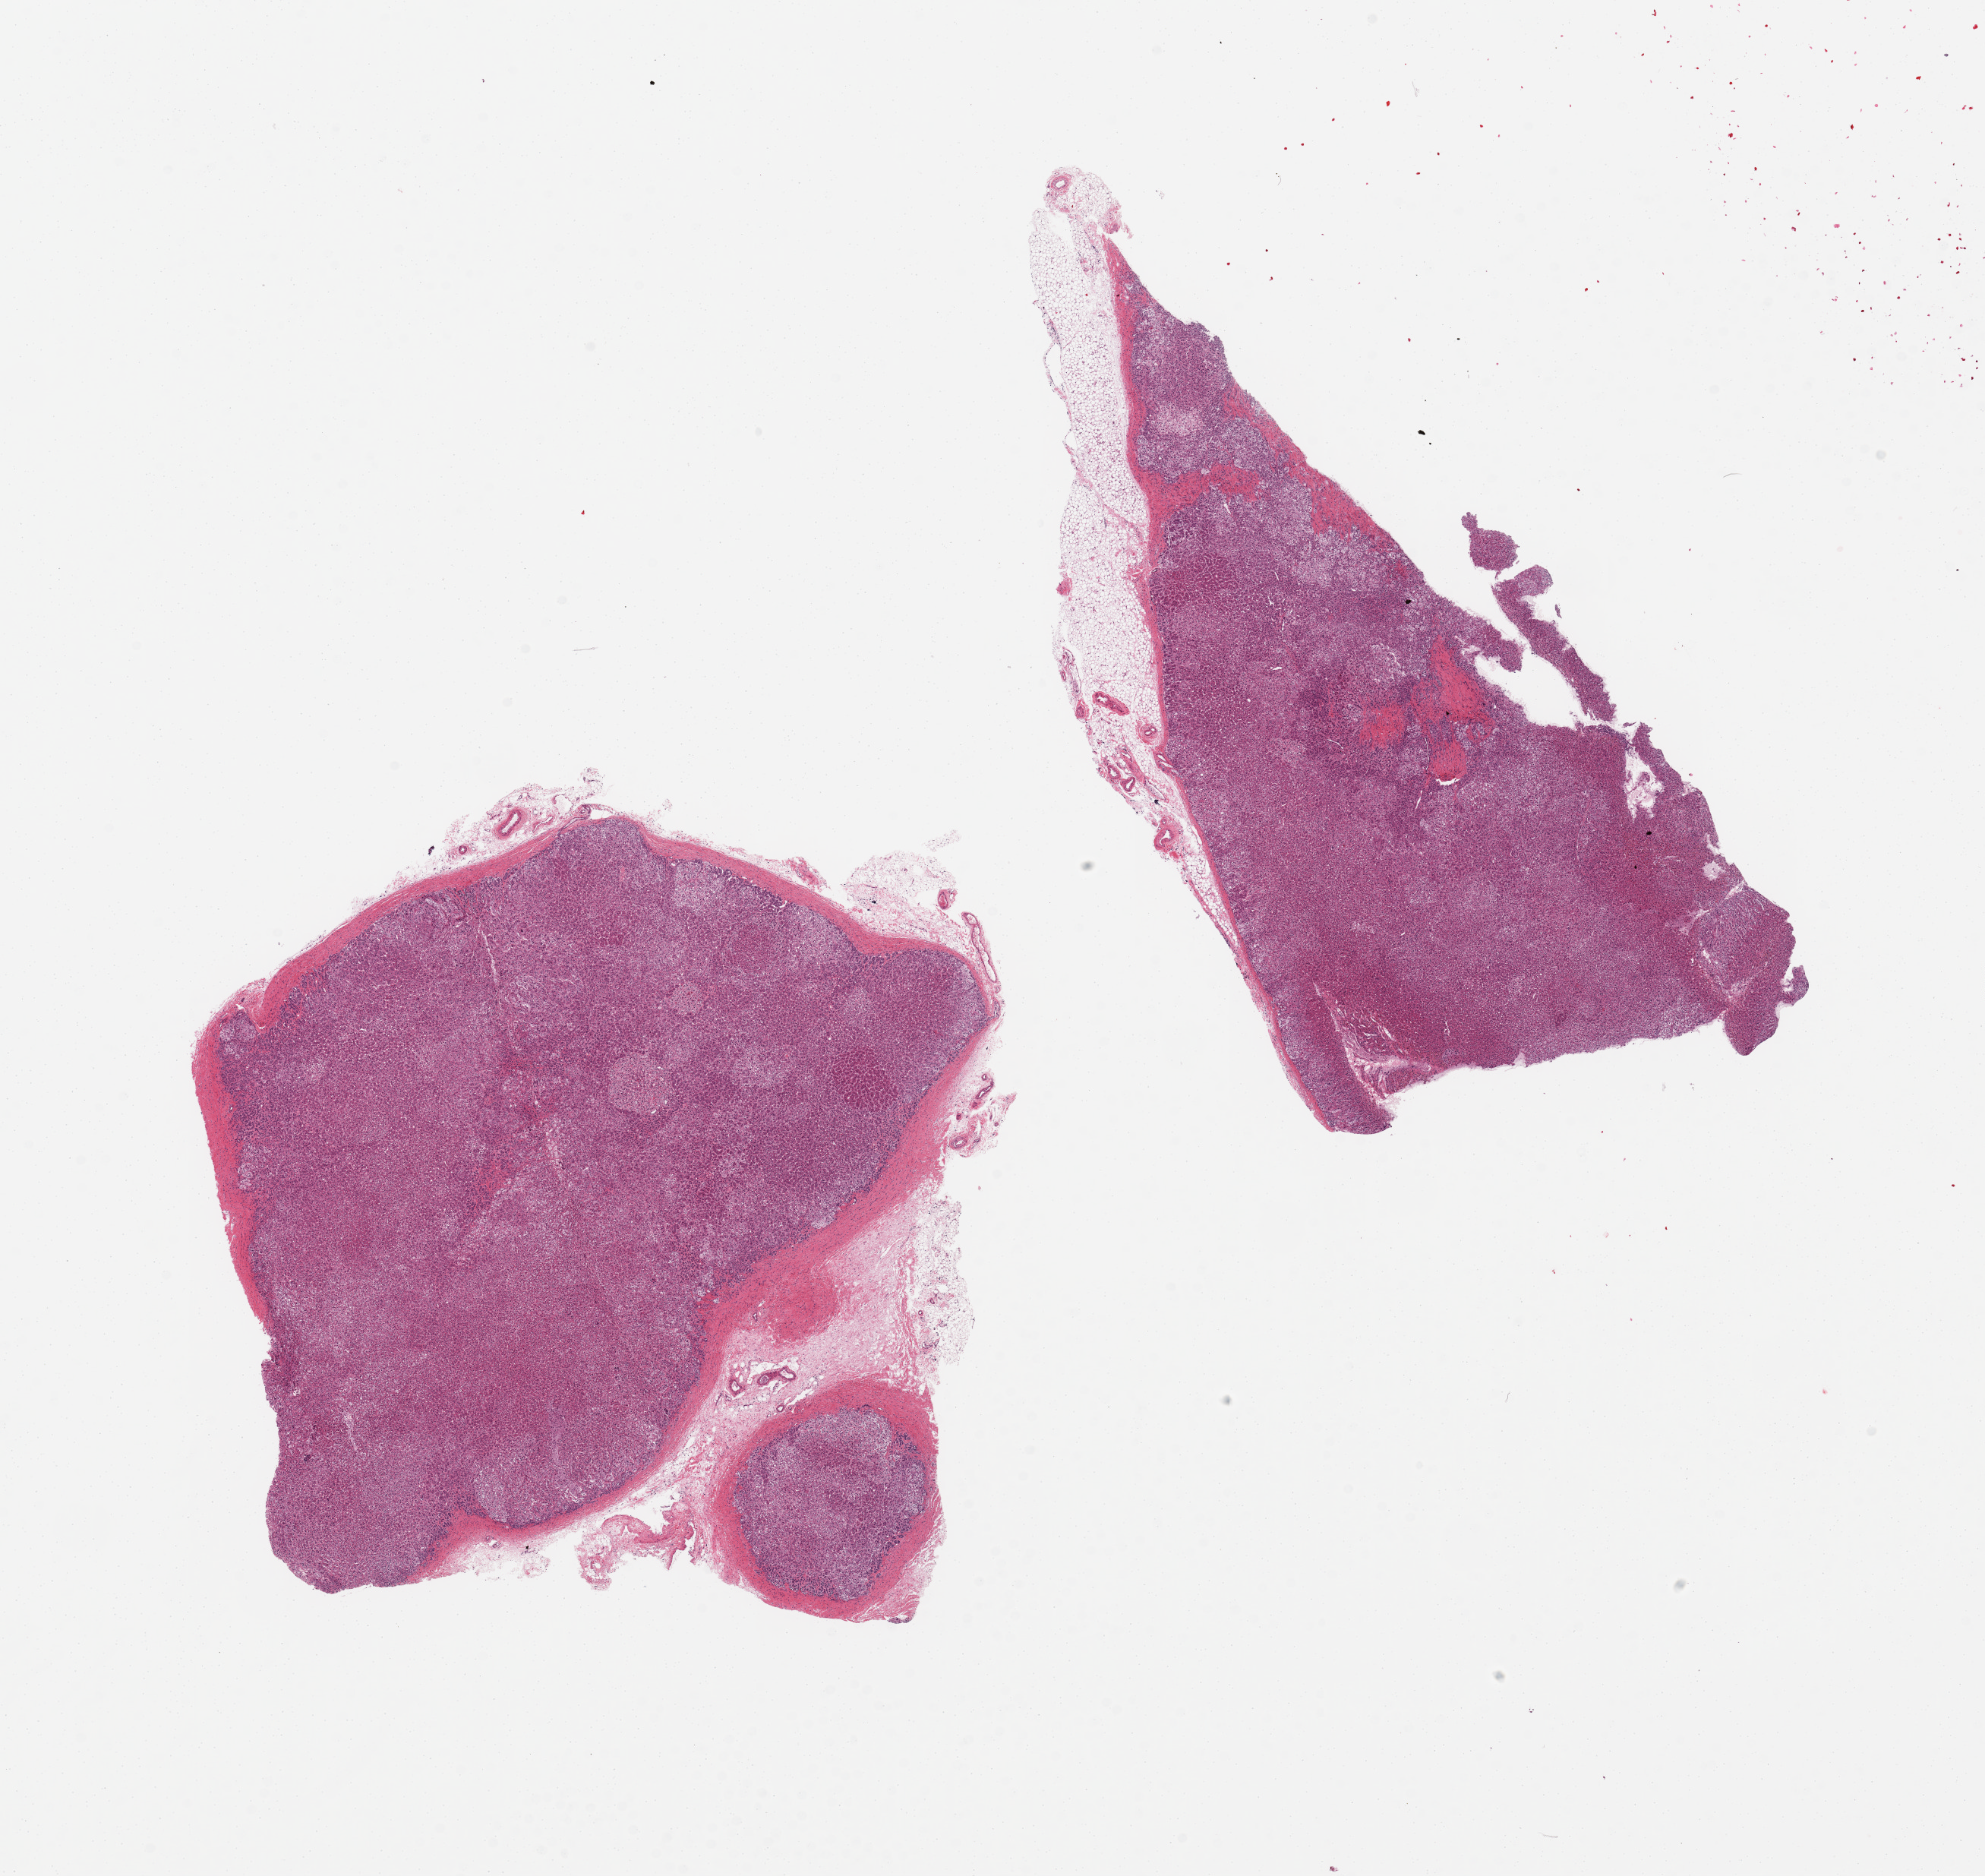
Digitized H&E-stained section — low-resolution overview of the scanned area, about 20.7 x 19.5 mm, PAXgene-fixed, paraffin-embedded tissue, sampled site (target tissue): adrenal gland, donor tissue sample. Donor: female.
- reviewer comment on this tissue sample: 2 pieces, up to 10% attached fibrofatty tissue